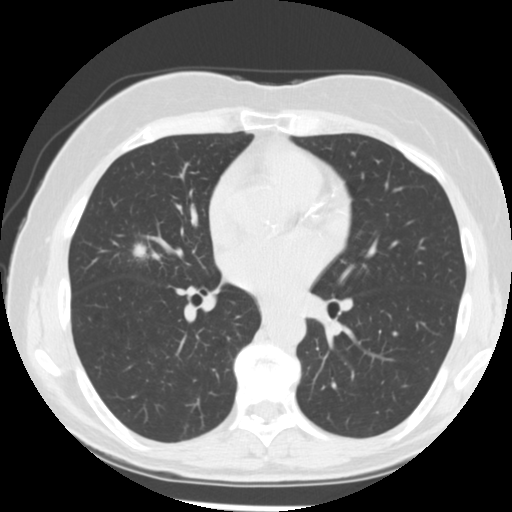
Low-dose screening chest CT, one axial slice. Position 138 of 255 along the scan axis. Lung window (W 1500 / L -600 HU). 512 × 512 image matrix, field of view 320 × 320 mm.
Outlined on this slice (manually delineated by an expert):
- lesion 1 (tumor, middle lobe of right lung): box from (x=133, y=243) to (x=147, y=258) px